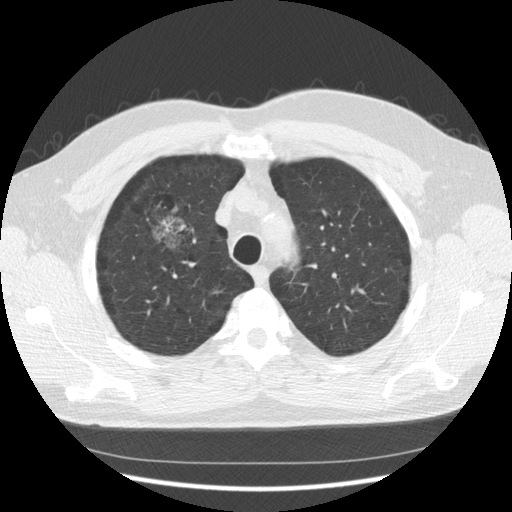
Low-dose screening chest CT, axial slice; third annual screen; lung window (W 1500 / L -600 HU); 2.5 mm slice thickness. Male, age 60 years at enrolment. Former smoker at enrolment.
Lesion marked by an expert reader, bounding box [x1, y1, x2, y2] px = [142, 204, 200, 267]. Screening reader's record for this exam (one nodule recorded; not confirmed to be the boxed lesion): non-calcified nodule or mass ≥4 mm, right upper lobe, poorly defined margins, mixed attenuation, pre-existing on the prior screen: yes; interval growth: yes. Lung cancer was diagnosed 121 days after this screen: papillary adenocarcinoma, NOS, right upper lobe, moderately differentiated (G2), stage IB (AJCC 6th edition), 32 mm at pathology.